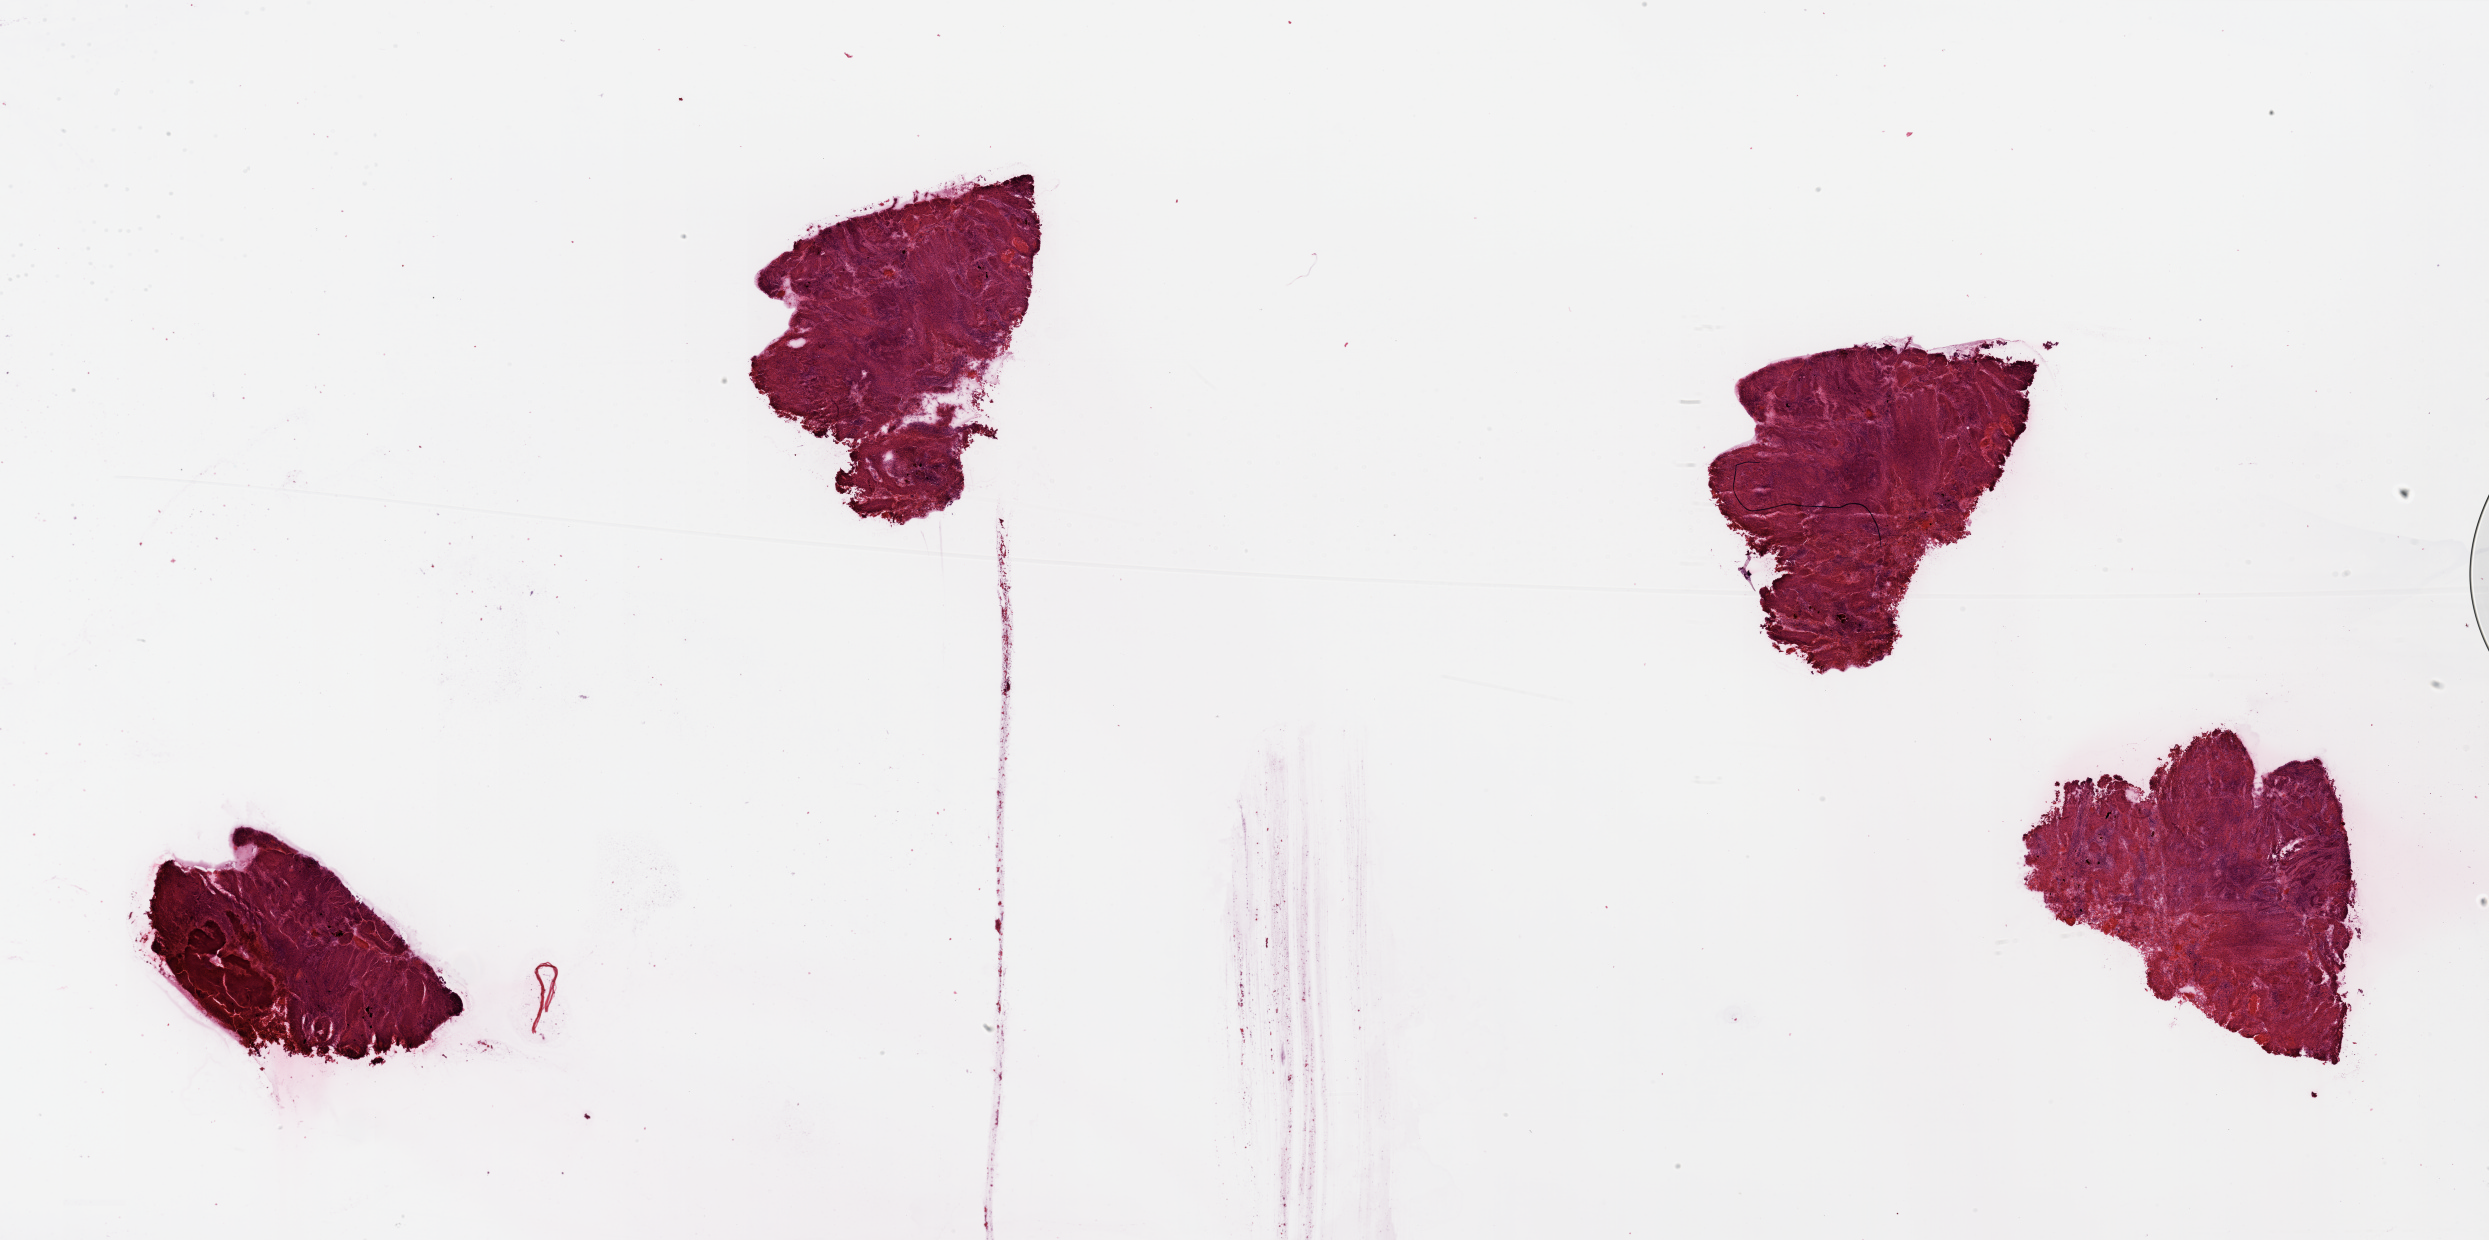
Whole-slide histology image, H&E, shown as a low-resolution overview of the whole scanned area (about 39.4 x 19.6 mm, slide scanned at 20x), tumour tissue sample, sampled site: larynx. Male, 69 y/o. Histologic grade: G2 (moderately differentiated). Slide review estimates, as recorded: tumour nuclei 90%, necrosis 5%.
* AJCC pathologic stage: II
* histologic diagnosis: Squamous cell carcinoma, NOS (larynx, NOS)